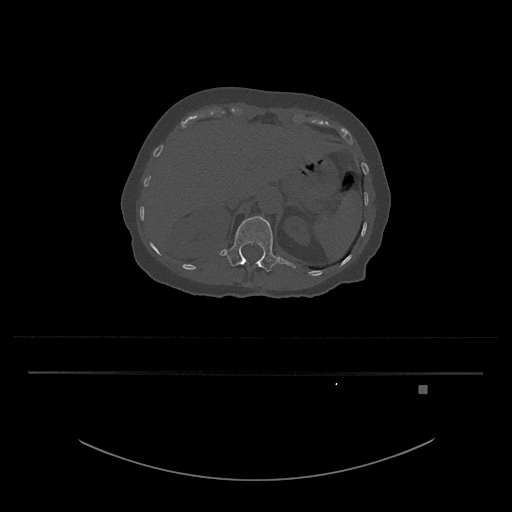
CT including the spine, one axial slice; position 561 of 797 along the scan axis; reconstruction kernel Br40s/3; 120 kVp; bone window (W 1800 / L 400 HU); 0.5 mm slice thickness; 512 × 512 image matrix, field of view 500 × 500 mm. Patient: female, 57 years. From the clinical record (not read from this slice): primary cancer: cervical.
Outlined on this slice (semi-automatically segmented with operator editing):
- L1 vertebra: bounding box [x1, y1, x2, y2] px = [219, 216, 296, 272]